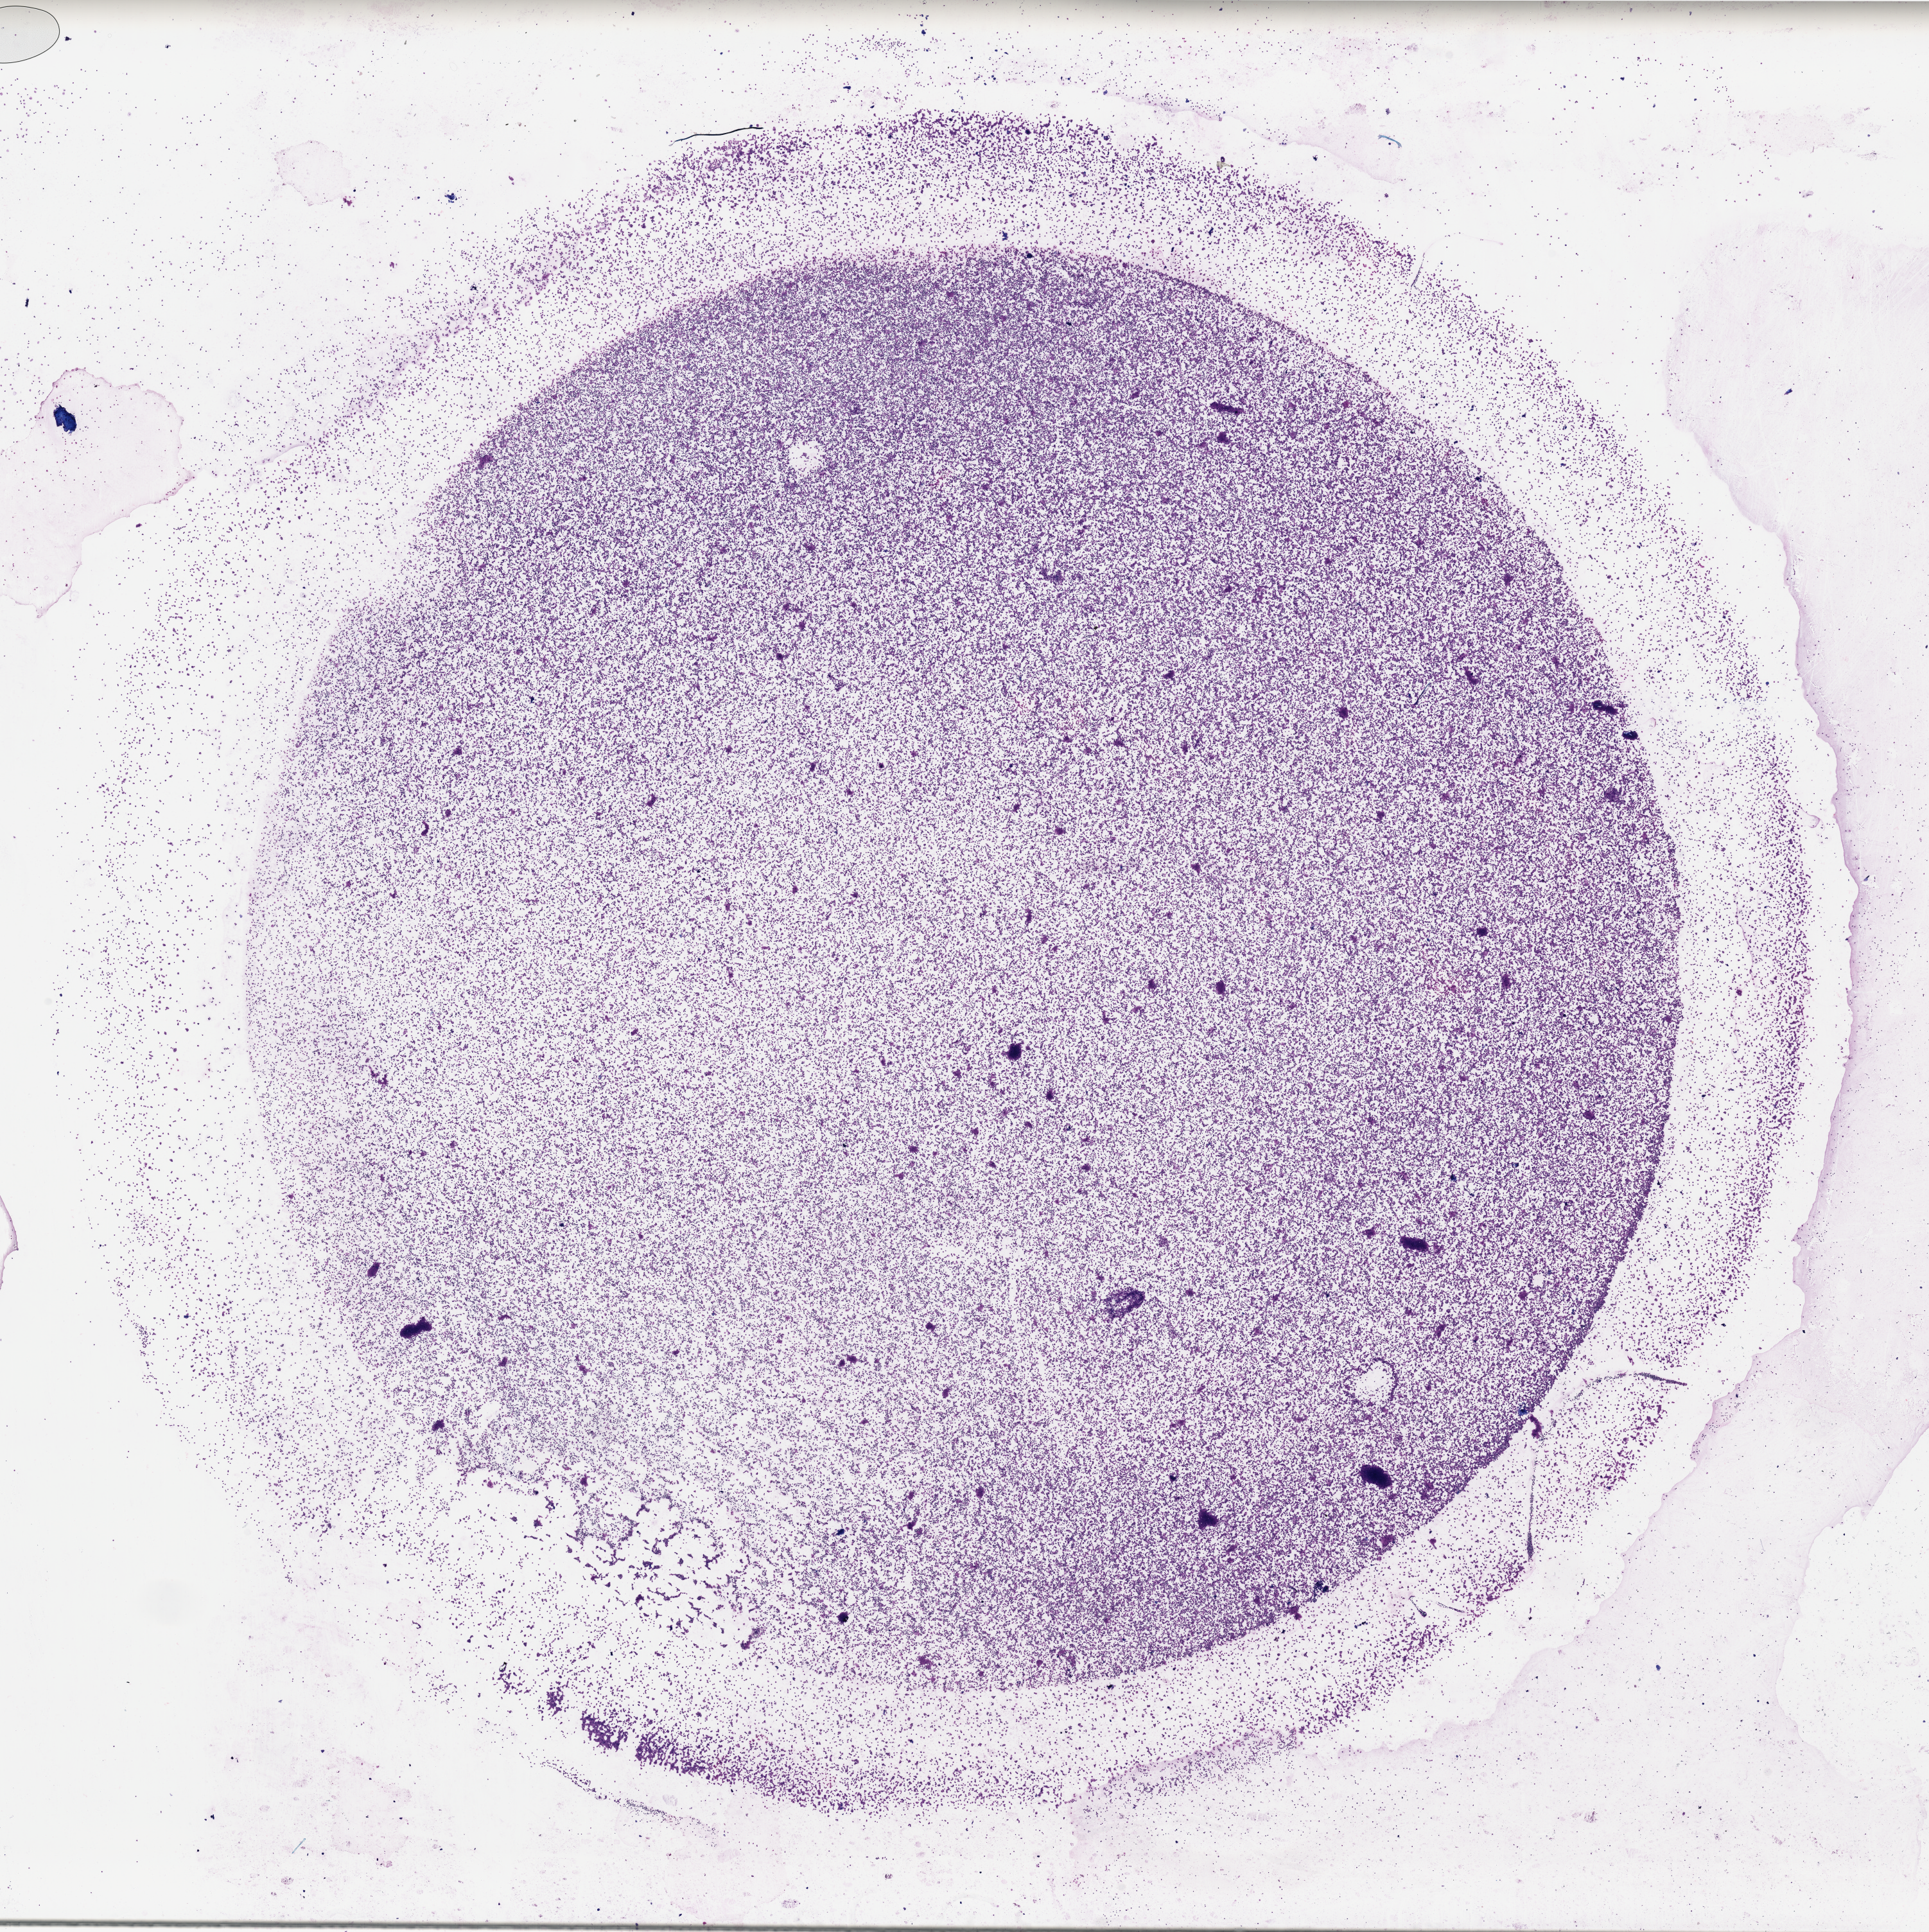
Whole-slide histology image, H&E-stained, whole scanned area (about 23.7 x 23.8 mm, acquisition: 40x scan) shown as a low-resolution overview. Bone marrow (leukaemic) sample. Patient: female, age 39 years. Blasts: 80%.
• diagnosis: Acute Myeloid Leukemia
• FAB classification: M0
• WHO classification: AML with minimal differentiation